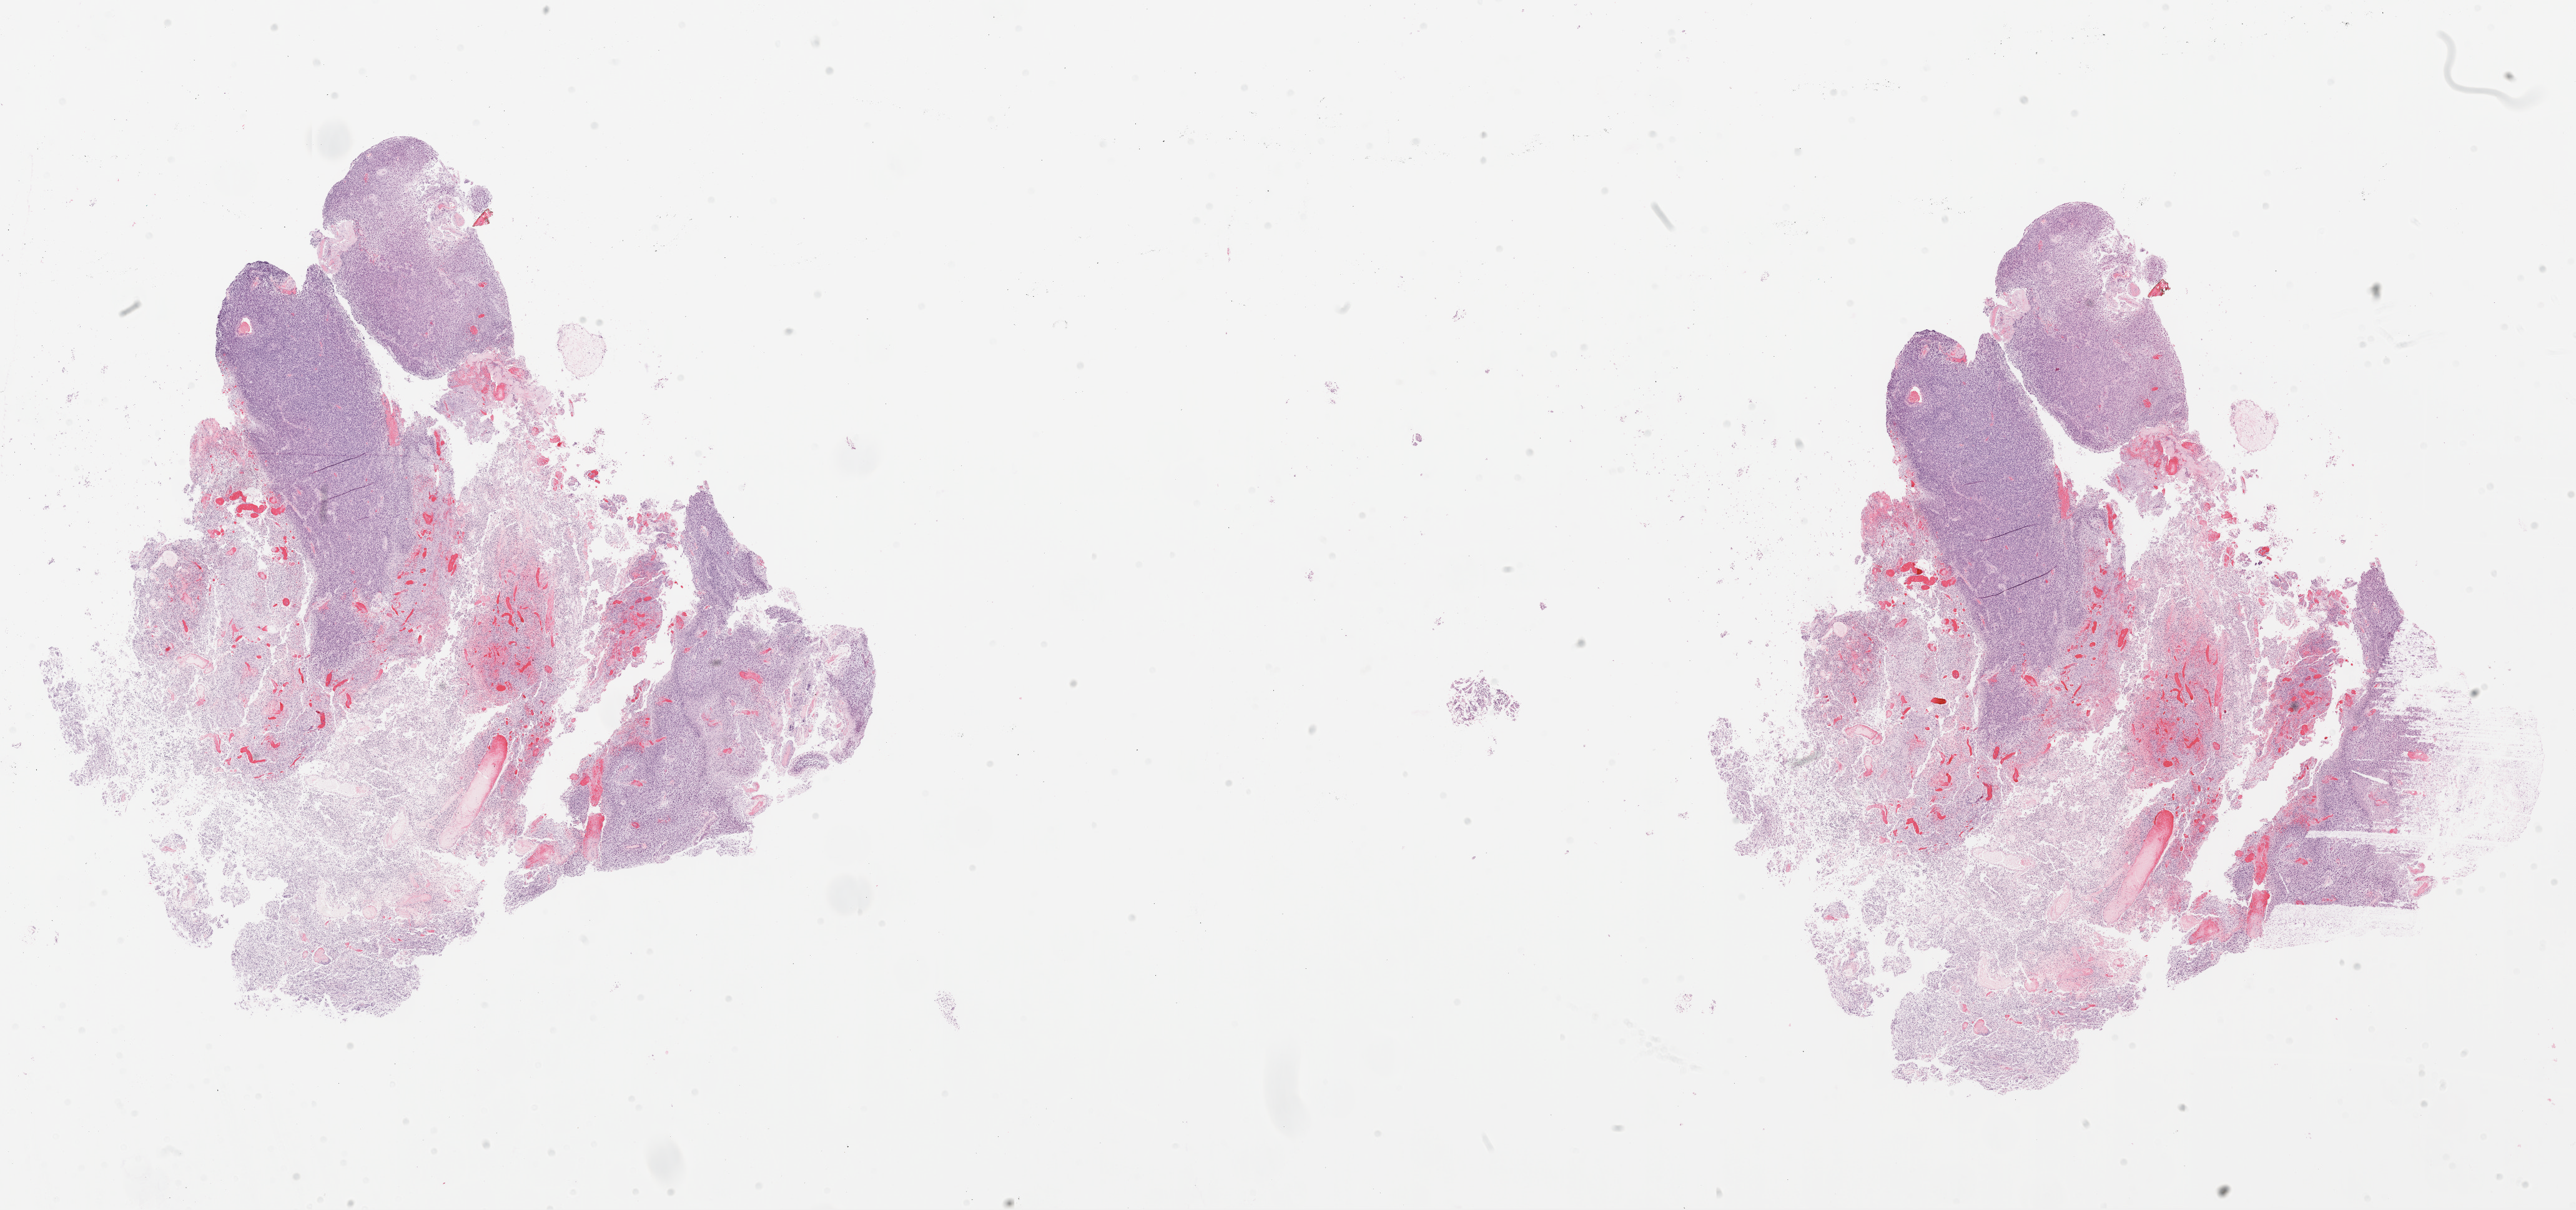
Digitized H&E tissue section (whole slide) — whole scanned area (about 33.1 x 15.5 mm) shown as a low-resolution overview. Formalin-fixed paraffin-embedded (FFPE) diagnostic section. Primary tumour sample from the brain. Male, age 52 years at initial diagnosis.
Histologic diagnosis: Glioblastoma.